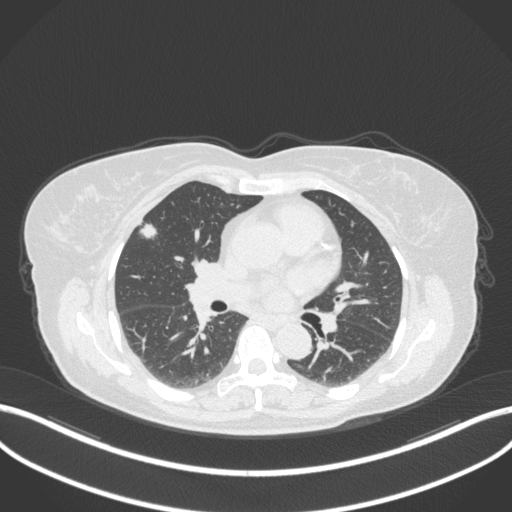
Chest CT, one axial slice; position 182 of 310 along the scan axis; reconstruction kernel B31f; 120 kVp; lung window (W 1500 / L -600 HU); 512 × 512 image matrix. Patient: female, 55 years. Case-level facts recorded for this patient, not image findings: clinical TNM (as recorded): T1b N0 M0; histopathological grade: G2.
Annotated regions visible in this slice (bounding box drawn by a radiologist):
- lung tumour (recorded histology: adenocarcinoma): bounding box [x1, y1, x2, y2] px = [133, 218, 159, 246]